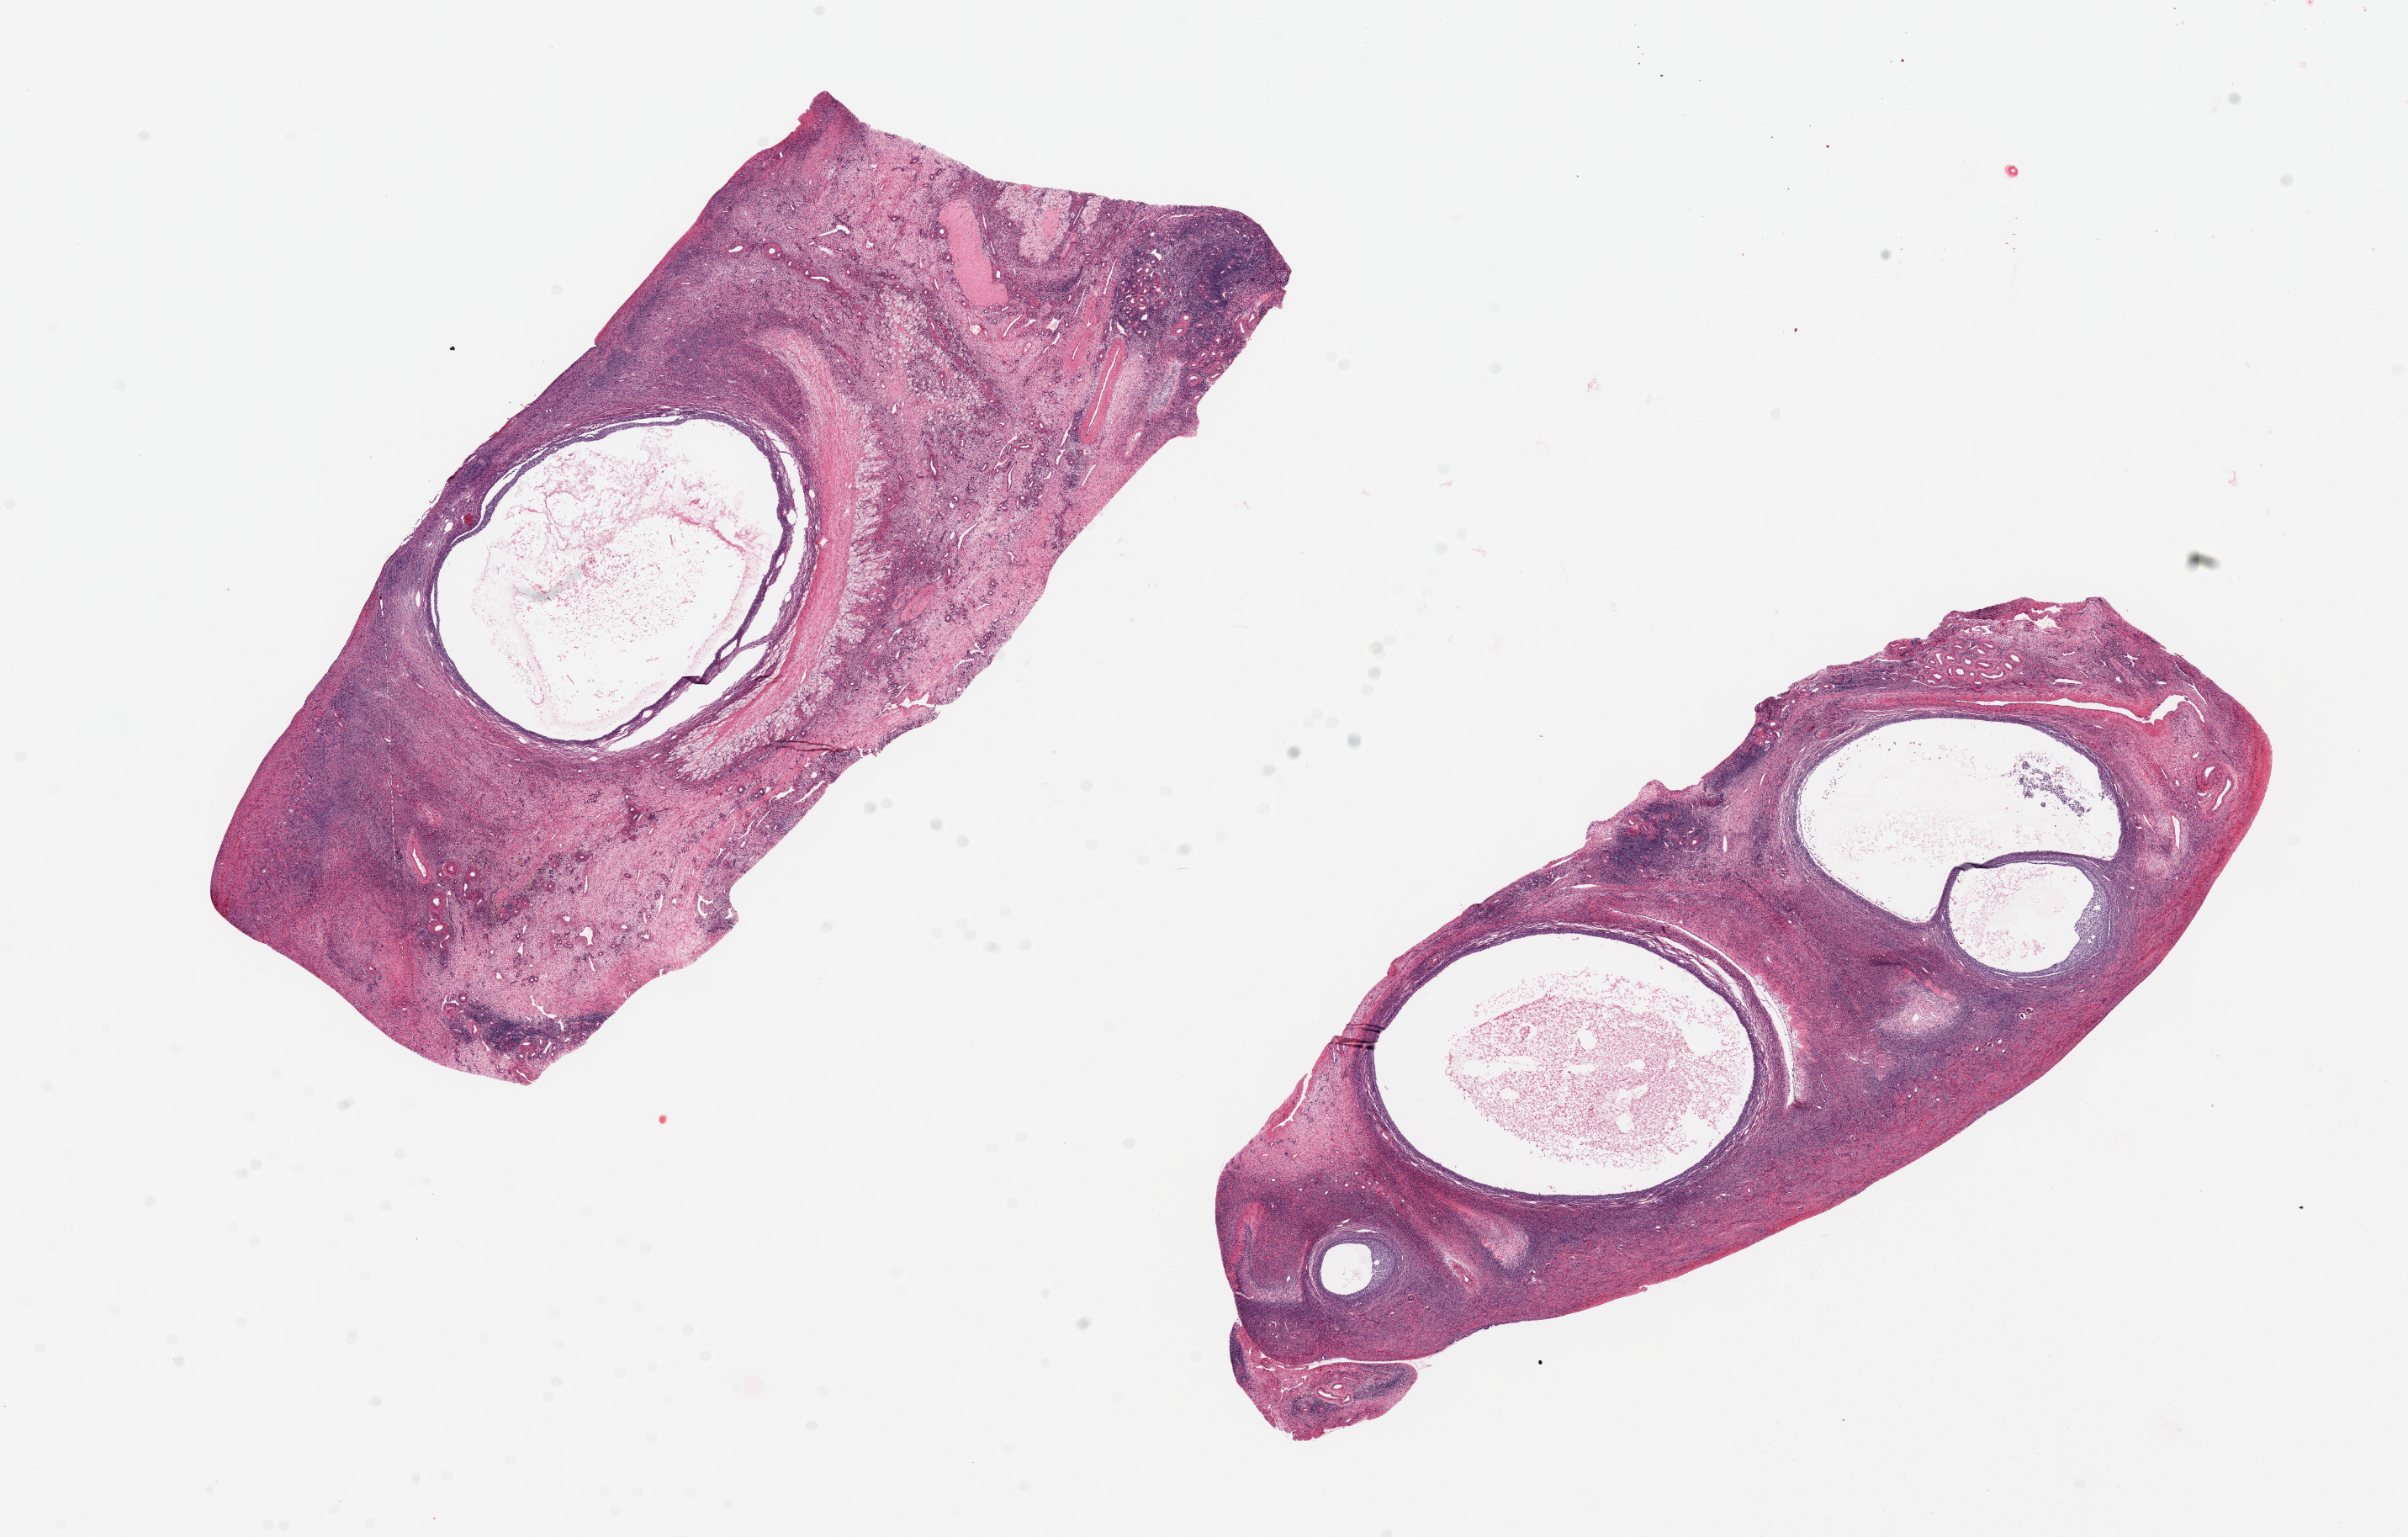
Digitized haematoxylin and eosin-stained section, low-resolution overview of the scanned area, about 22.6 x 14.4 mm. PAXgene-fixed, paraffin-embedded tissue. Sampled site (target tissue): ovary. Donor tissue sample. Donor: female.
Pathologist's review note for this sample: 2 pieces, 10x4 mm; numerous ova and follicles in various stages of normal function.